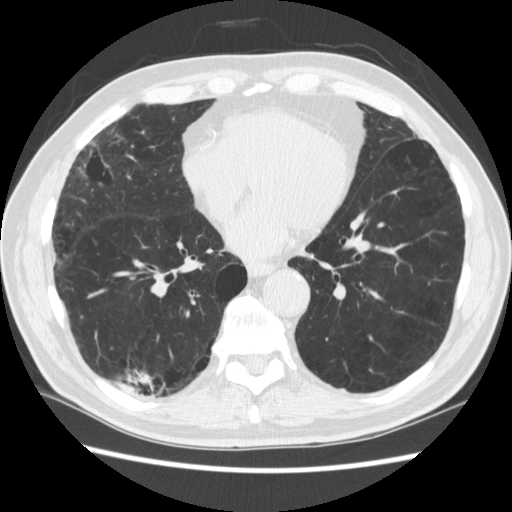
Chest CT (low-dose screening protocol), one axial image, third annual screen, lung window (W 1500 / L -600 HU), 1.25 mm slice thickness, standard (soft-tissue) reconstruction kernel (STANDARD), 512 × 512 image matrix, field of view 360 × 360 mm. Male, age 70 years at enrolment. Former smoker at enrolment.
• Expert reader's lesion annotation, bounding box <128,359,179,414> (left, top, right, bottom; pixels).
• The screening reader recorded 4 non-calcified nodules or masses ≥4 mm on this exam; which of them this box marks is not recorded.
• Official screen result: positive, other.
• Participant outcome: lung cancer diagnosed 253 days after this screen — squamous cell carcinoma, NOS, right upper lobe, poorly differentiated (G3), stage IV (AJCC 6th edition).